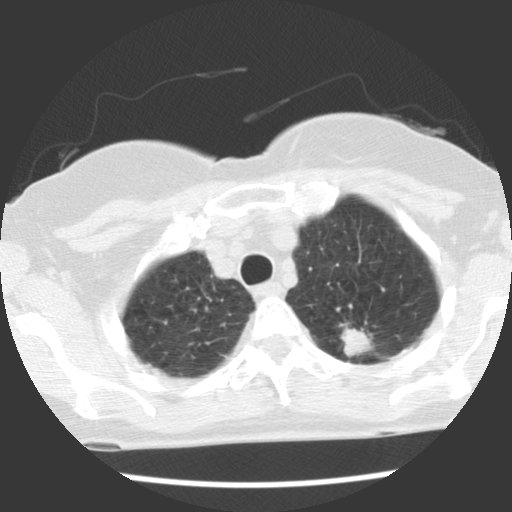
Axial slice from a low-dose chest CT screening exam, first (baseline) screen, lung window (W 1500 / L -600 HU), 2.5 mm slice thickness, 512 × 512 image matrix, field of view 300 × 300 mm. Female, age 66 years at enrolment.
- Lesion marked by an expert reader, box from (x=319, y=308) to (x=388, y=371) px.
- Screening reader's record for this exam (one nodule recorded; not confirmed to be the boxed lesion): non-calcified nodule or mass ≥4 mm, left upper lobe, 22 × 17 mm, spiculated (stellate) margins, soft tissue attenuation.
- Later outcome: lung cancer diagnosed 50 days after this screen — adenocarcinoma, NOS, left upper lobe, poorly differentiated (G3), stage IB (AJCC 6th edition), 40 mm at pathology.